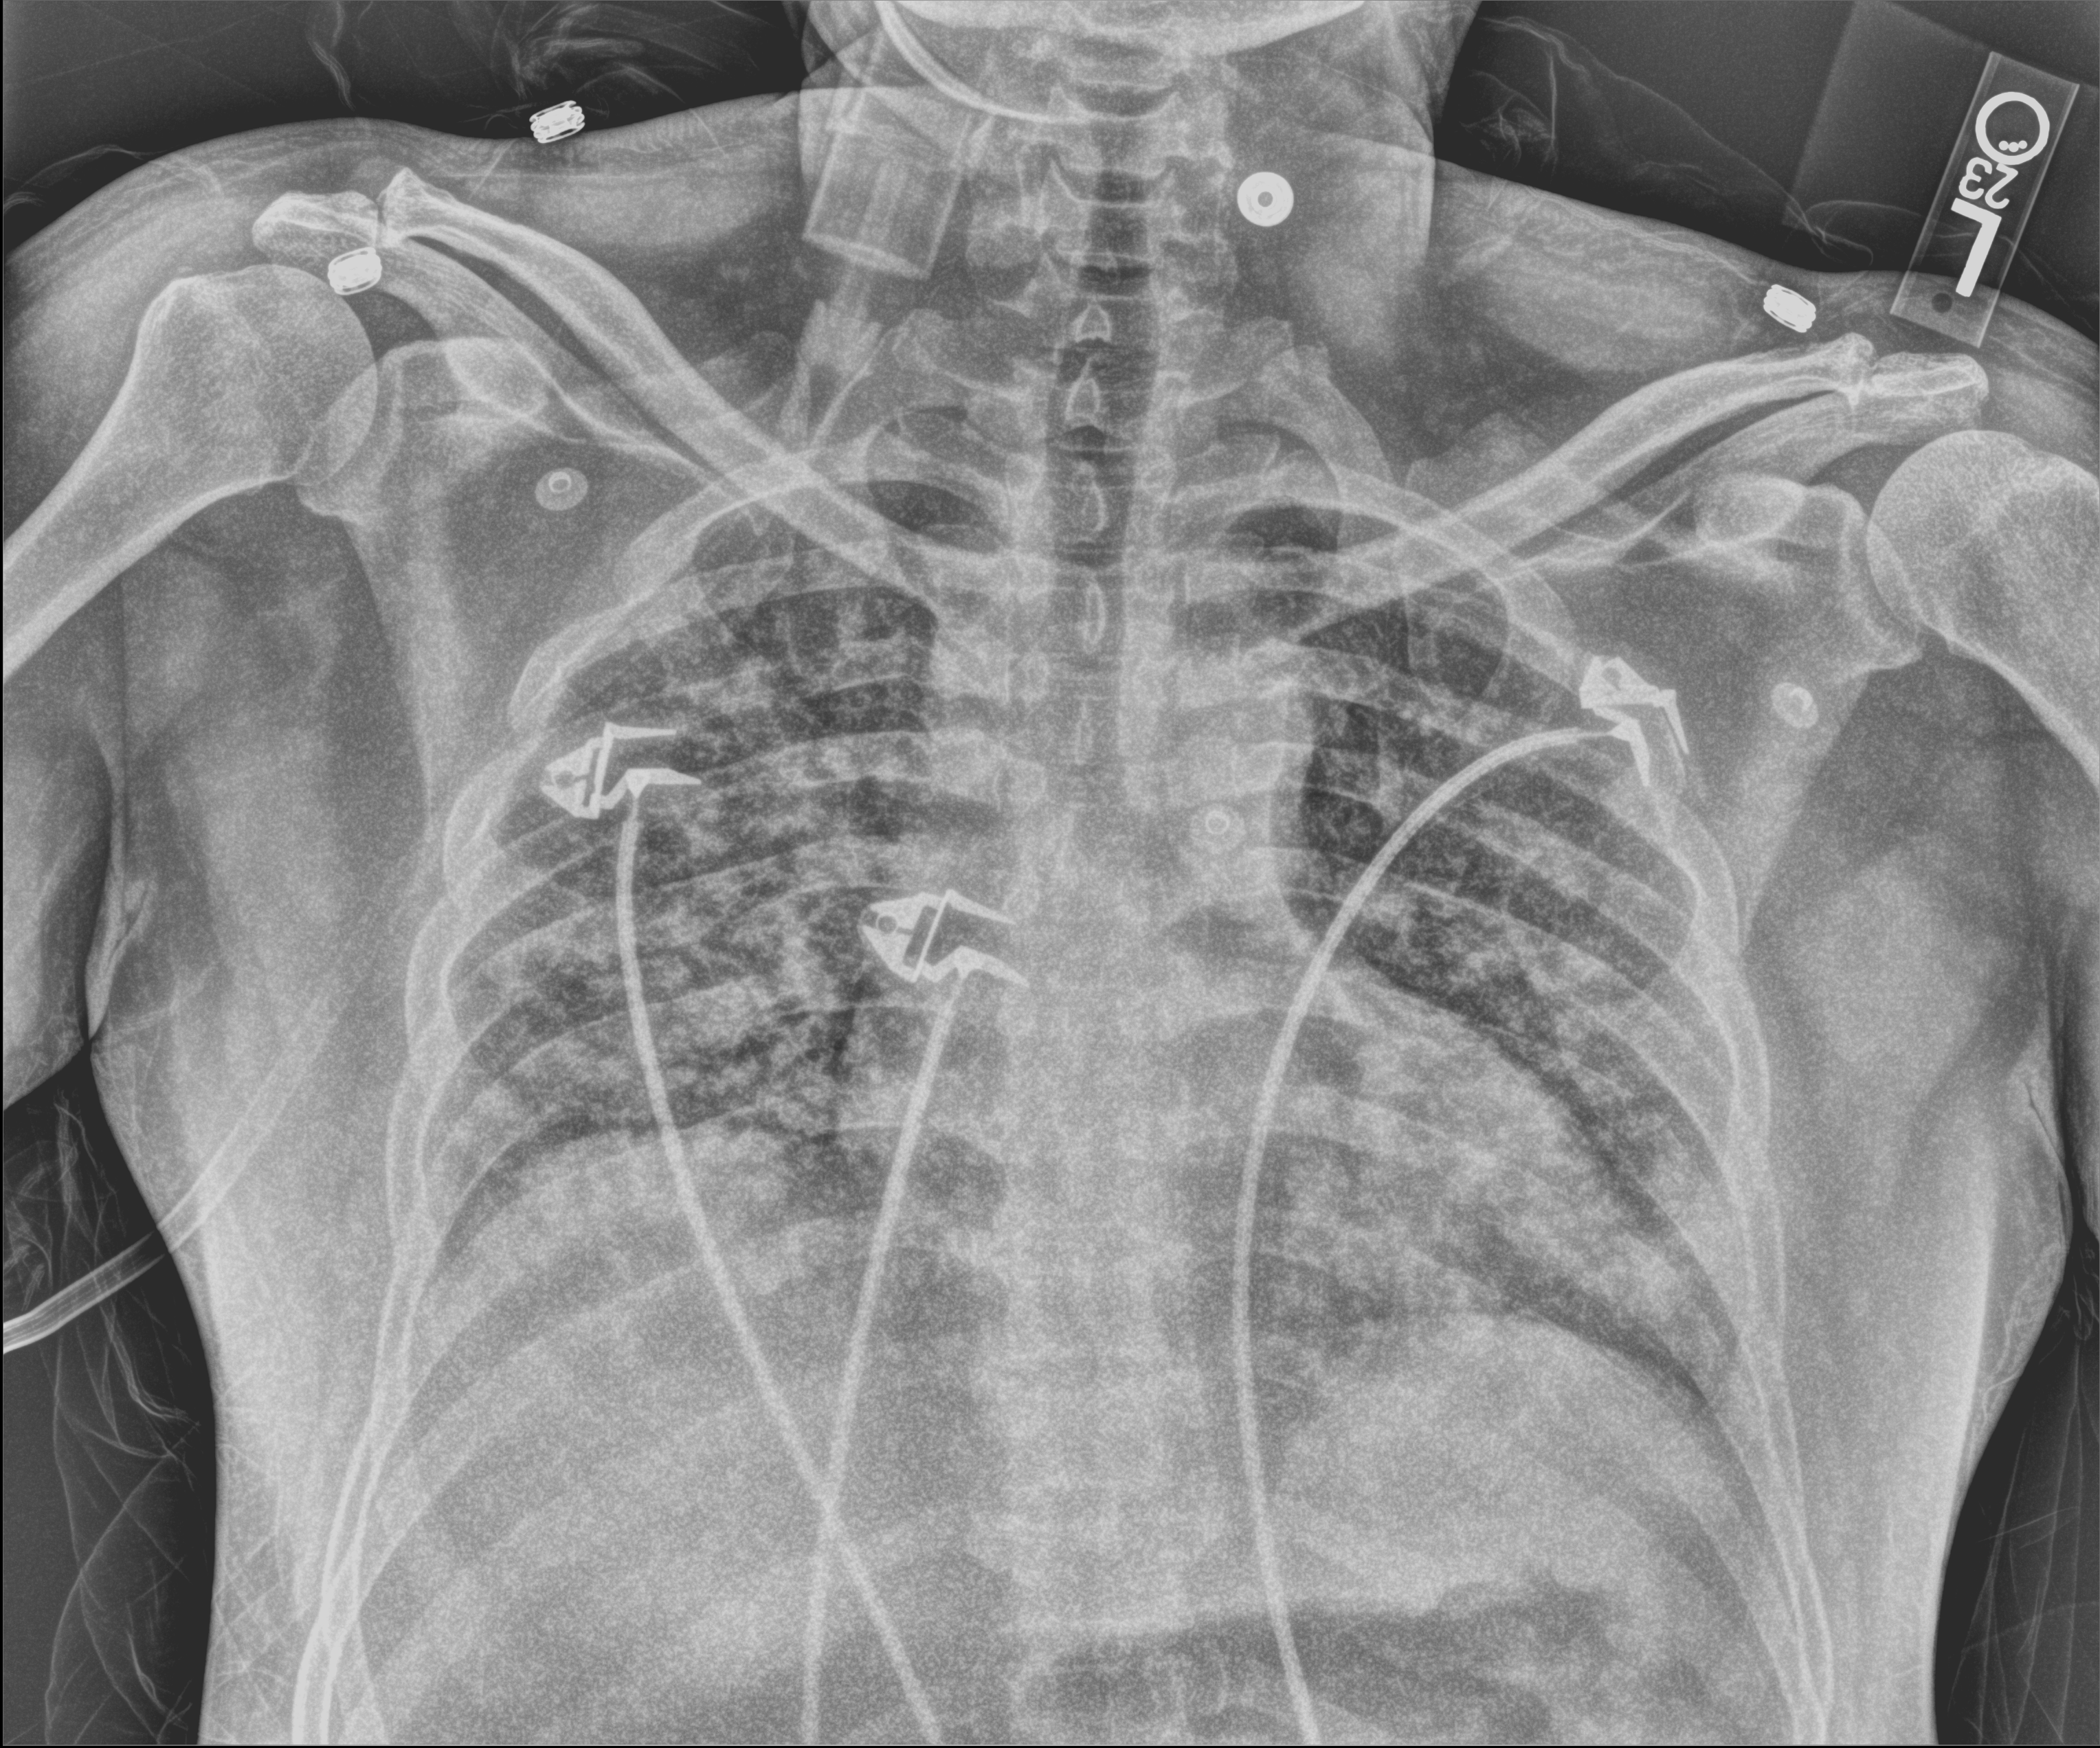
Bedside chest radiograph (computed radiography); anteroposterior (AP) projection. Patient hospitalised with COVID-19; male, aged 18–59 years.
Hospital-stay facts (about this admission, not read from this image; timing relative to this image not recorded):
- smoking status (admission record): never
- admitted to intensive care during this hospital stay: no